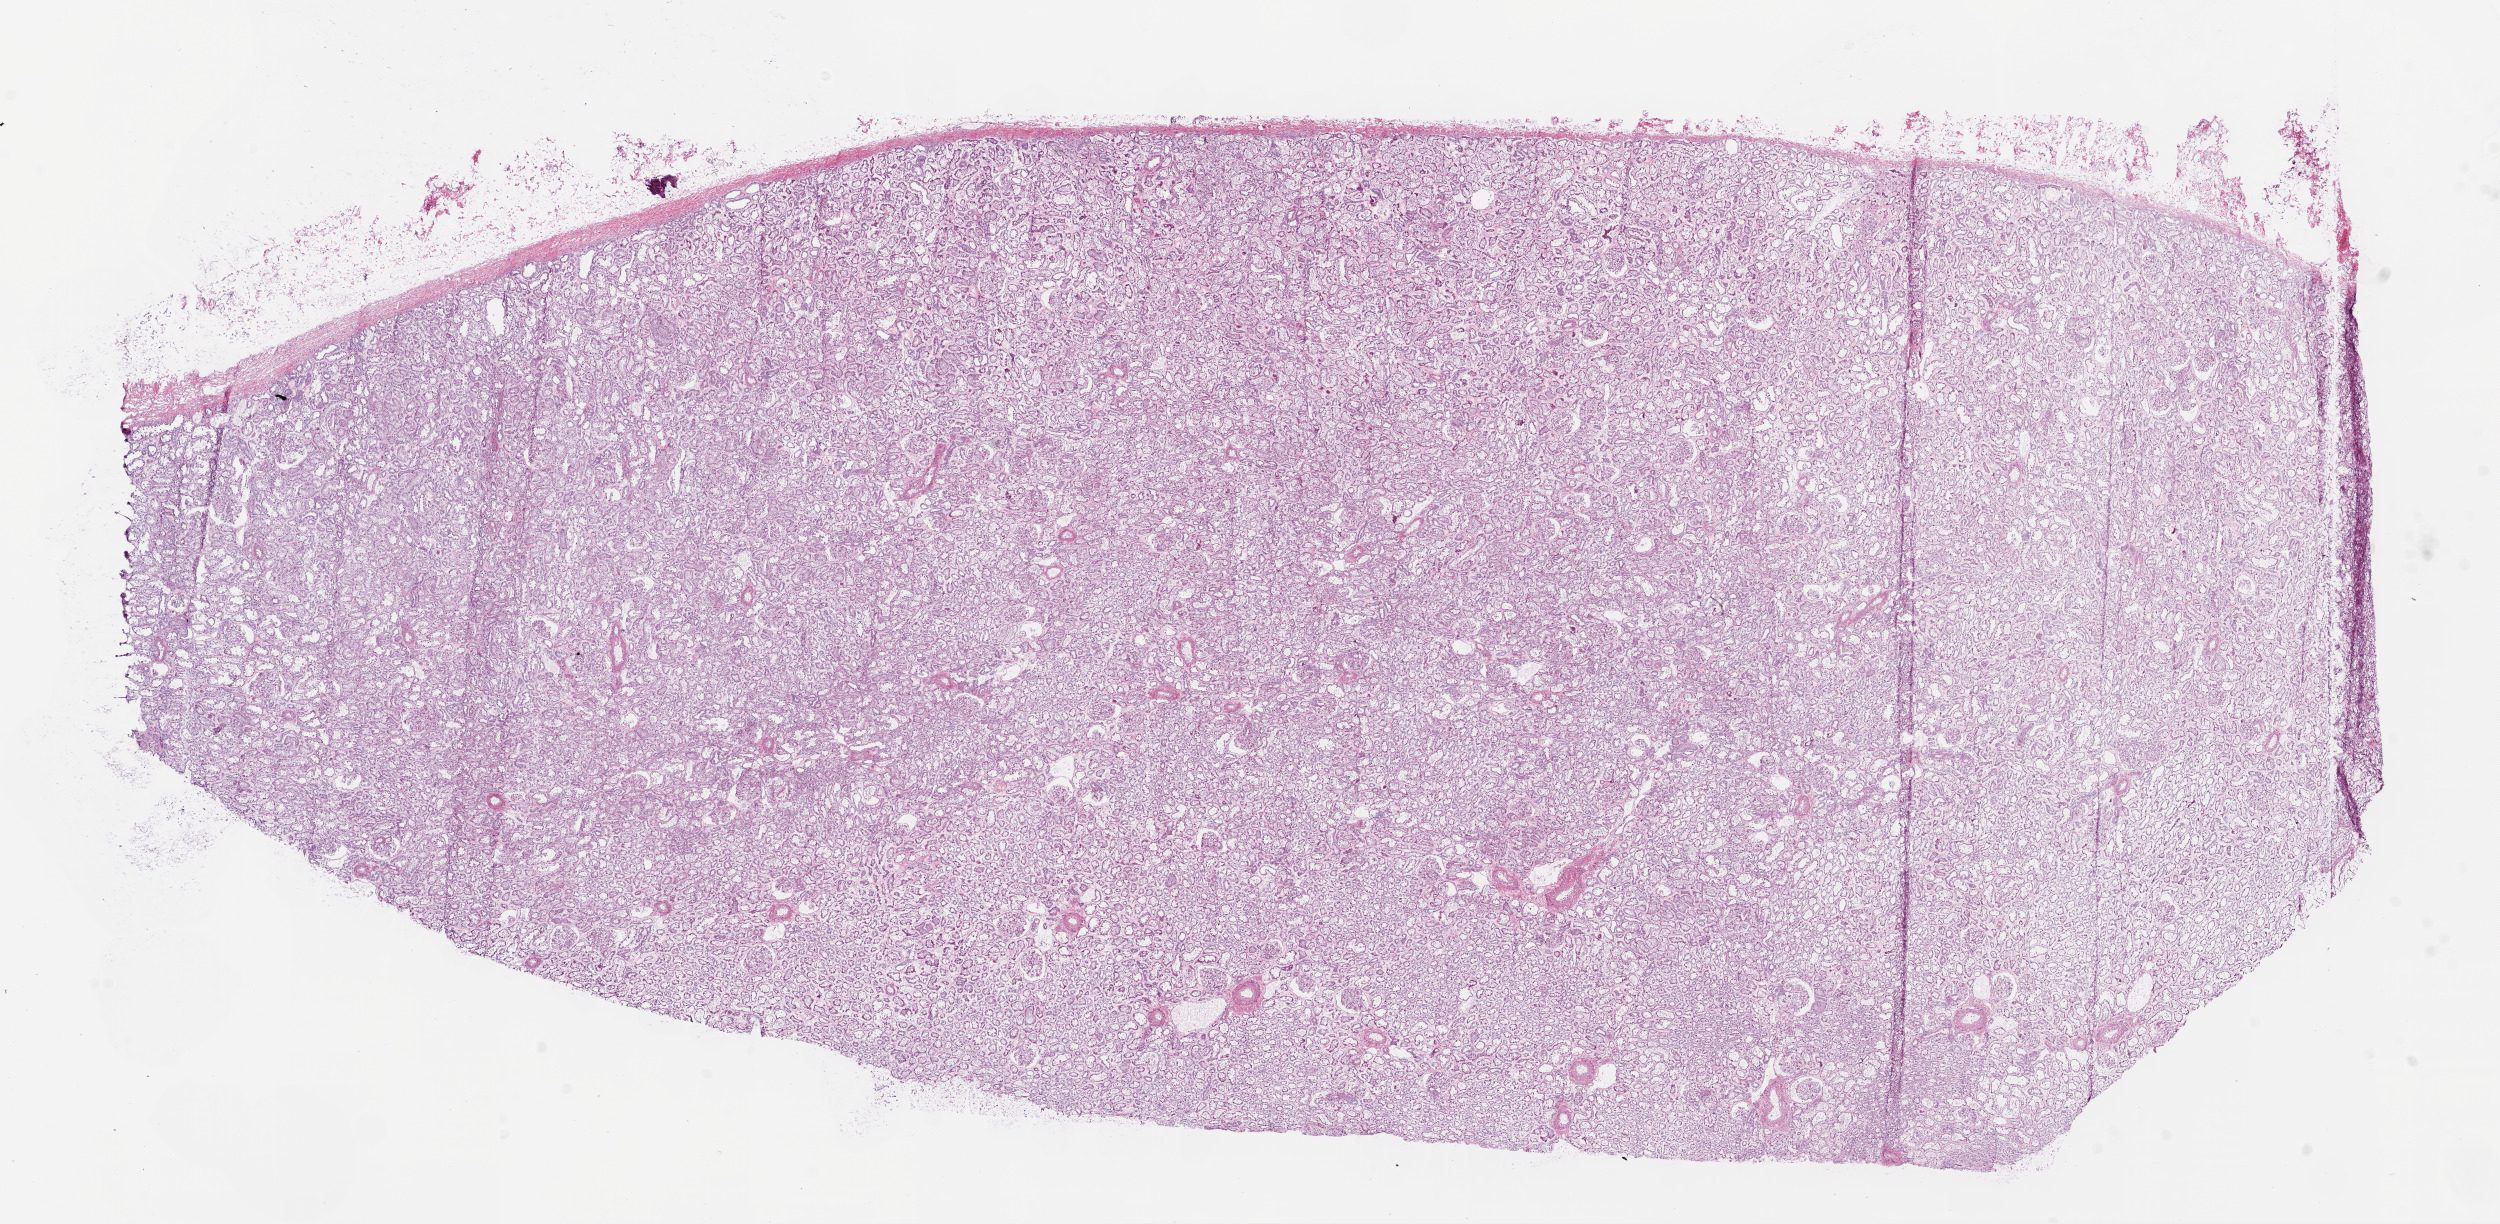
Digitized H&E-stained tissue section (whole slide) — low-resolution overview of the scanned area, about 20.1 x 9.8 mm (slide scanned at 20x), frozen section from the bottom of the tissue portion, solid tissue normal (non-tumour tissue) sample from the kidney. Male, age 61 years at initial diagnosis.
This section: solid tissue normal (non-tumour) sample from the same patient. Patient diagnosis: Clear cell adenocarcinoma, NOS.